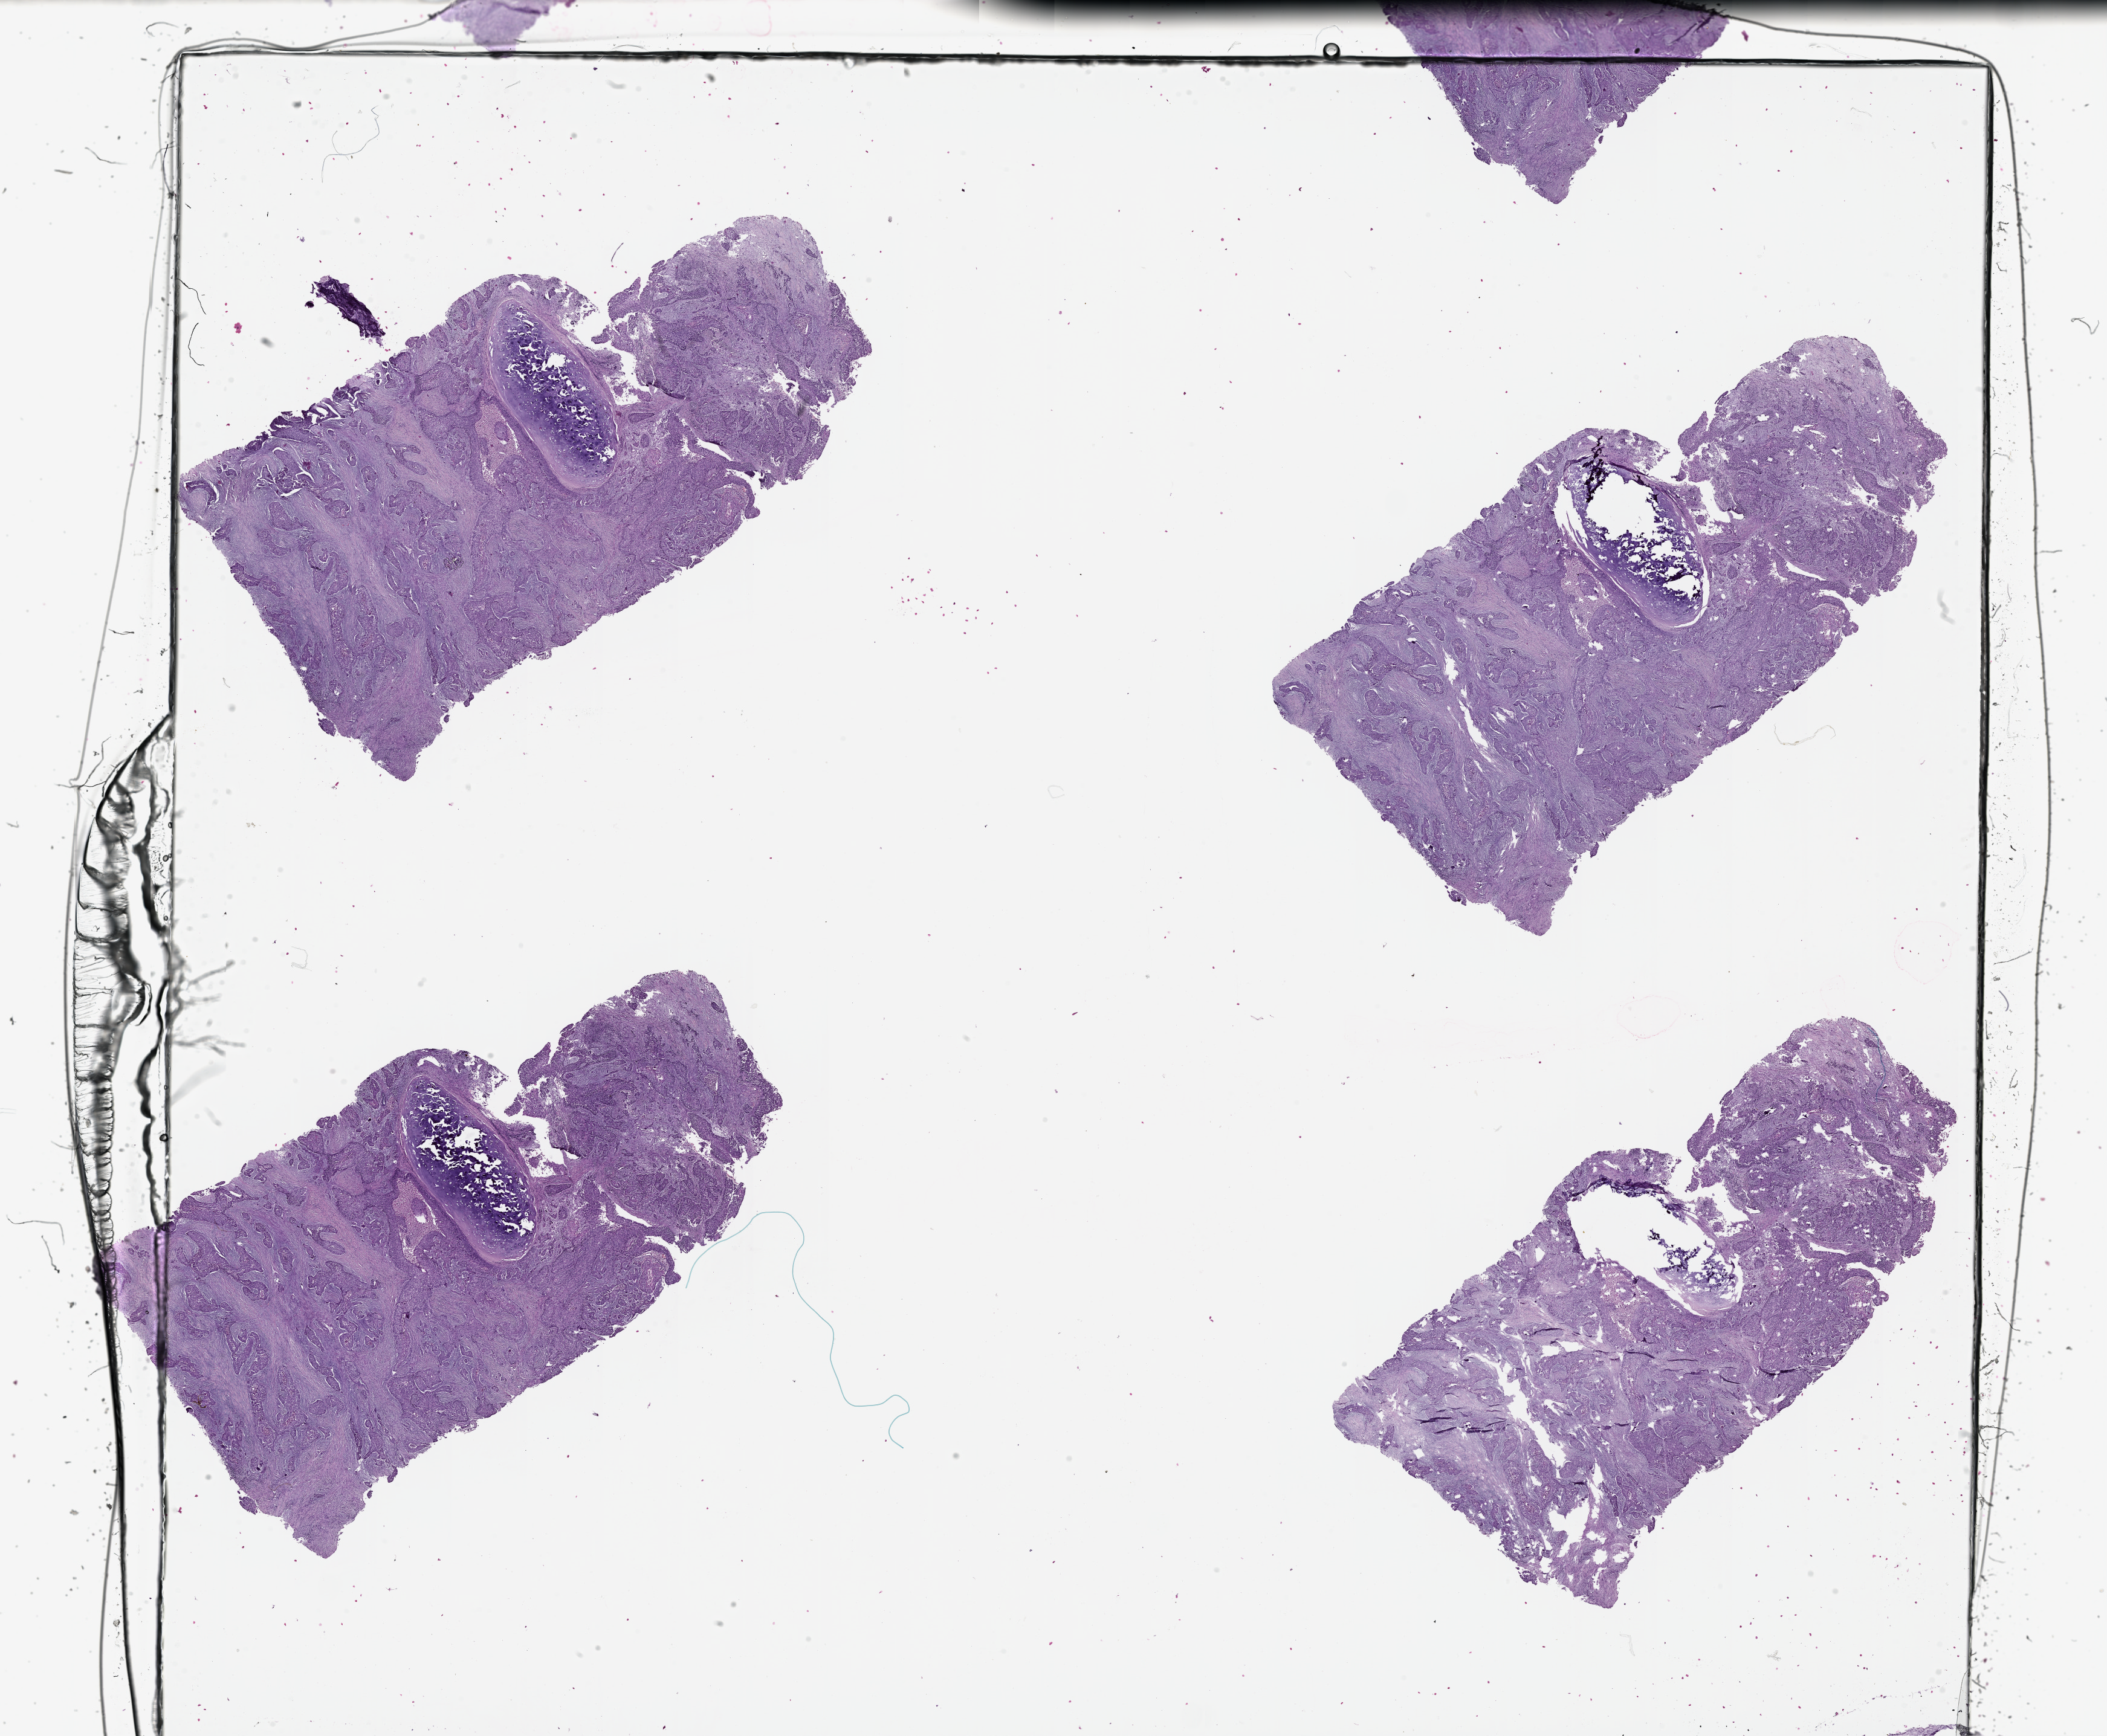
H&E whole-slide image, shown as a low-resolution overview of the whole scanned area (about 28.1 x 23.1 mm, acquisition: 20x scan); tumour tissue sample, lung. Male, 67 y/o.
Patient diagnosis (cohort enrolment): squamous cell carcinoma (lung).